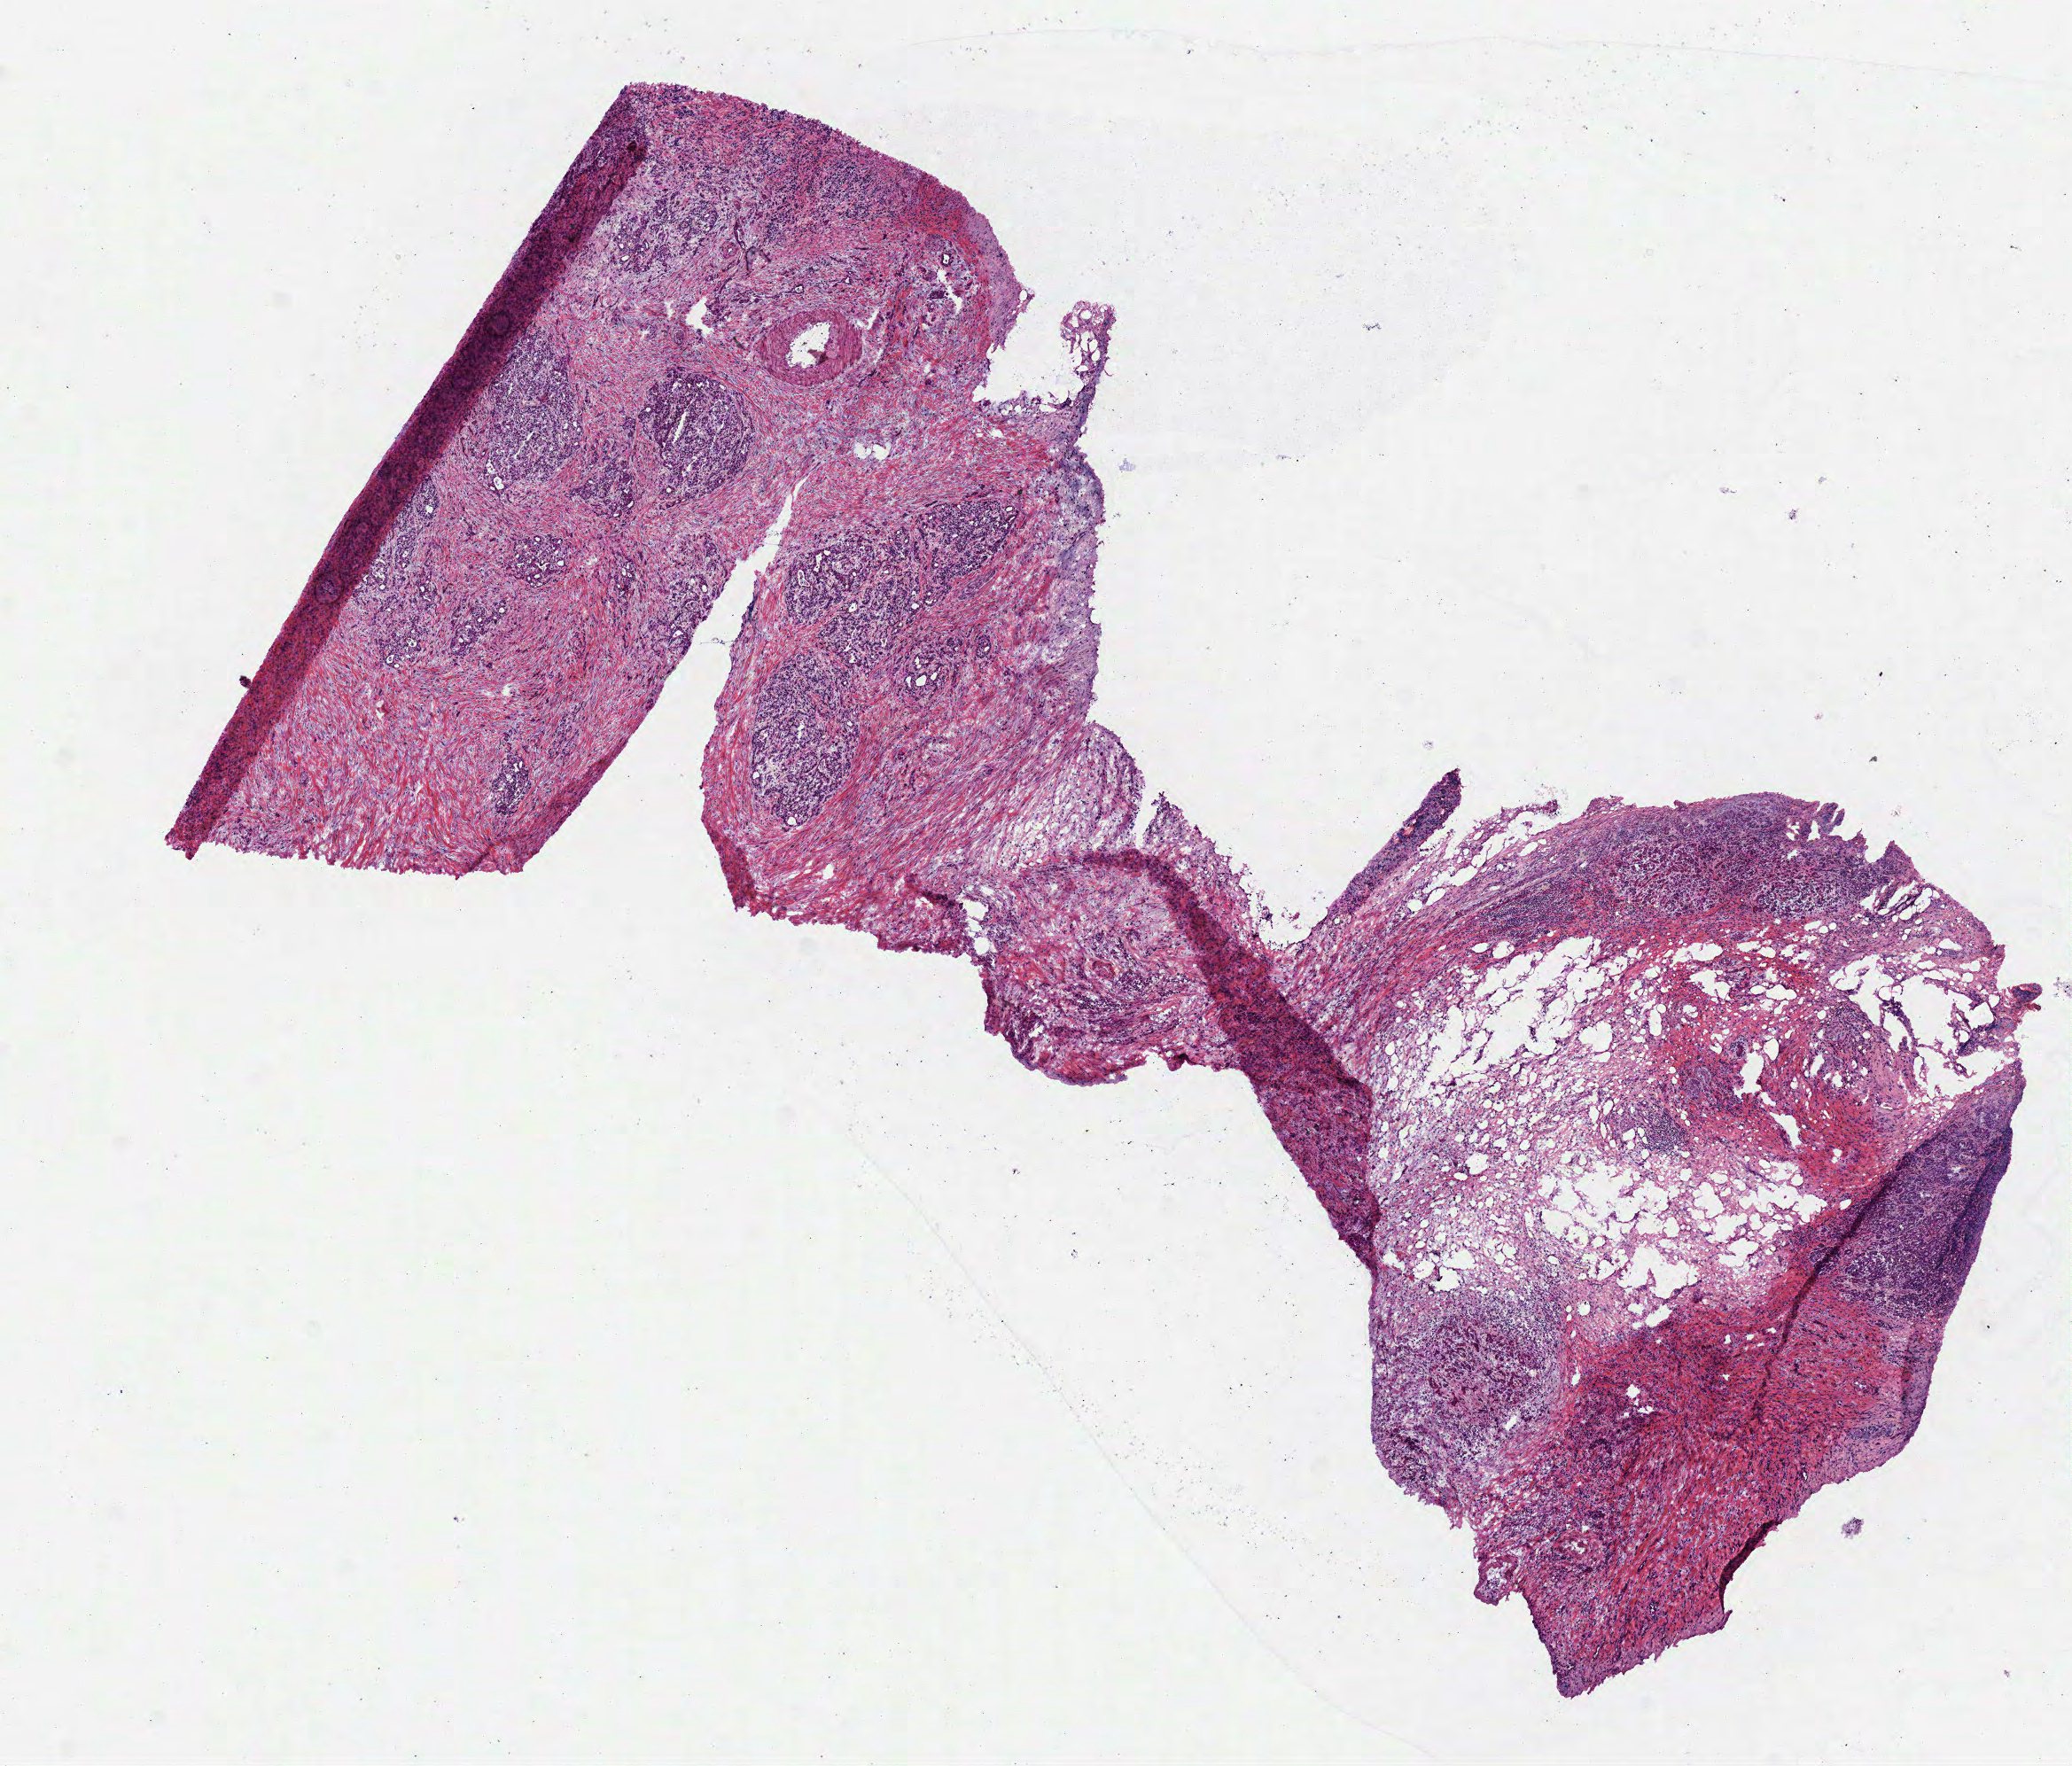
Whole-slide histology image, H&E-stained, whole scanned area (about 9.4 x 8.0 mm) shown as a low-resolution overview, frozen section, sample: primary tumour, pancreas. Male, age 73 years at initial diagnosis.
Diagnosis: Adenocarcinoma, NOS.